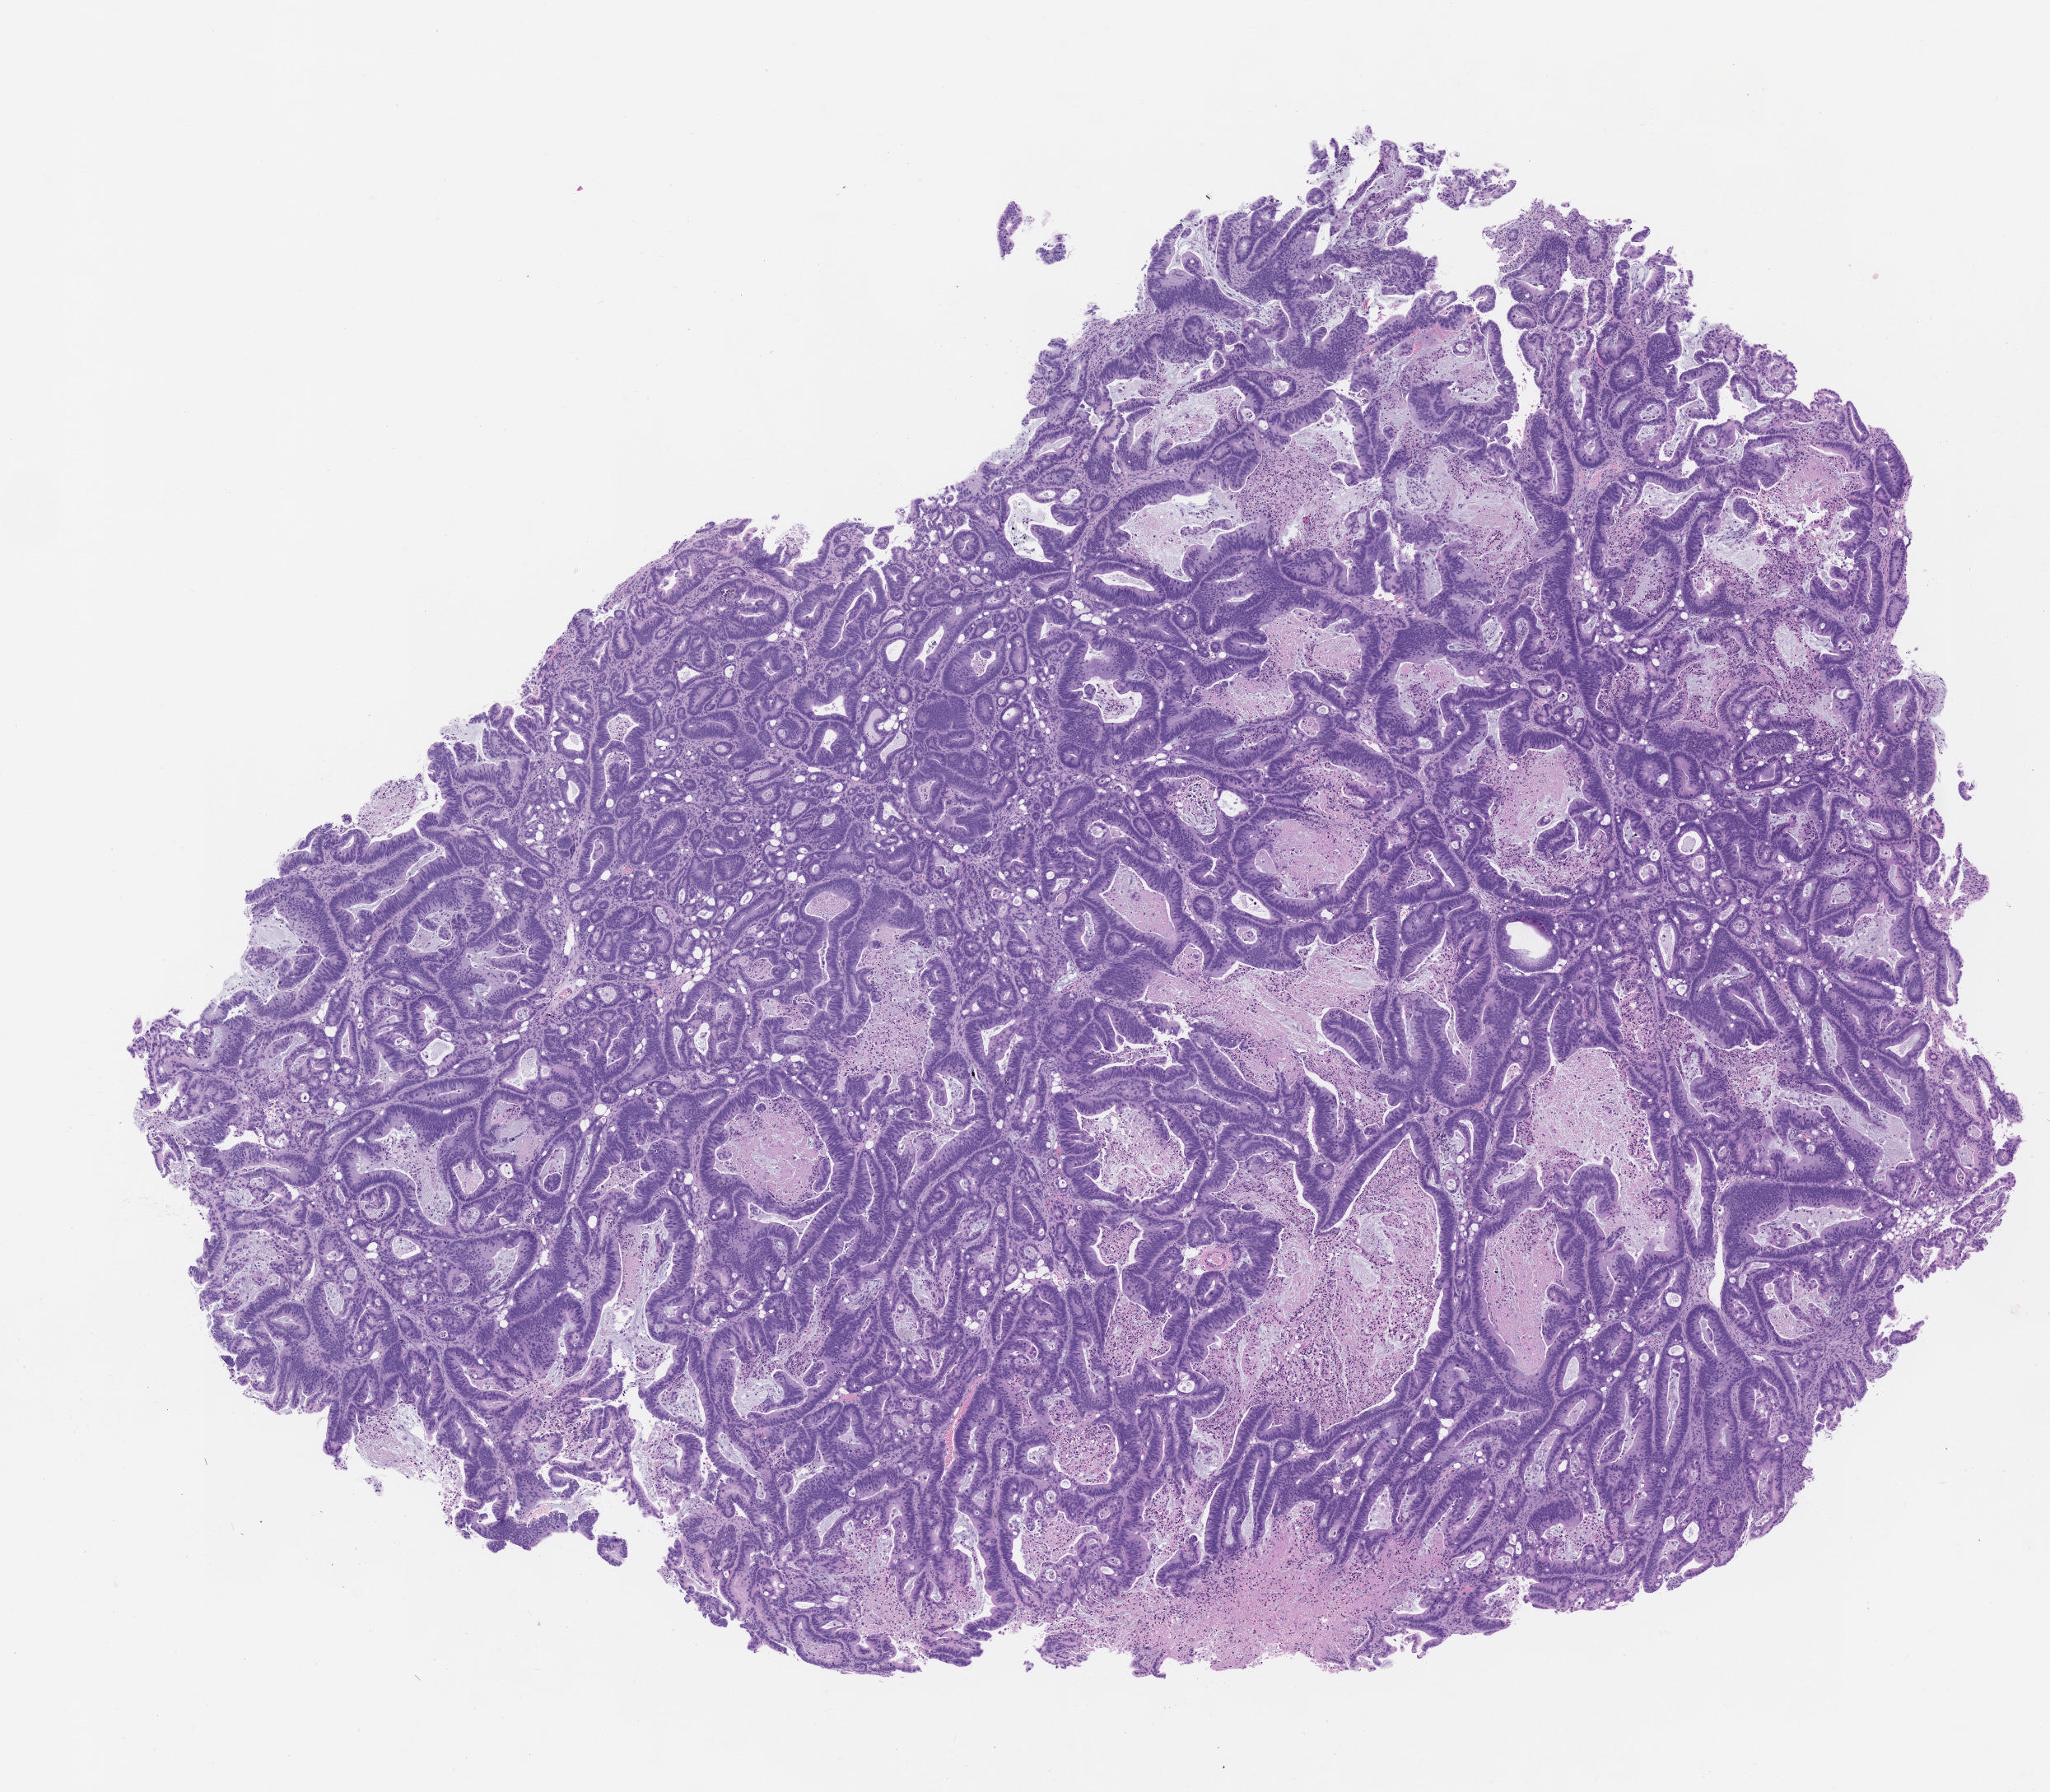
Whole-slide image, H&E: patient-derived xenograft (human tumor grown in a mouse), passage 2 — low-resolution overview of the scanned area, about 10.0 x 8.8 mm. Formalin-fixed paraffin-embedded section. Originating tumor site category: colon.
Originating patient diagnosis: Colon Adenocarcinoma.